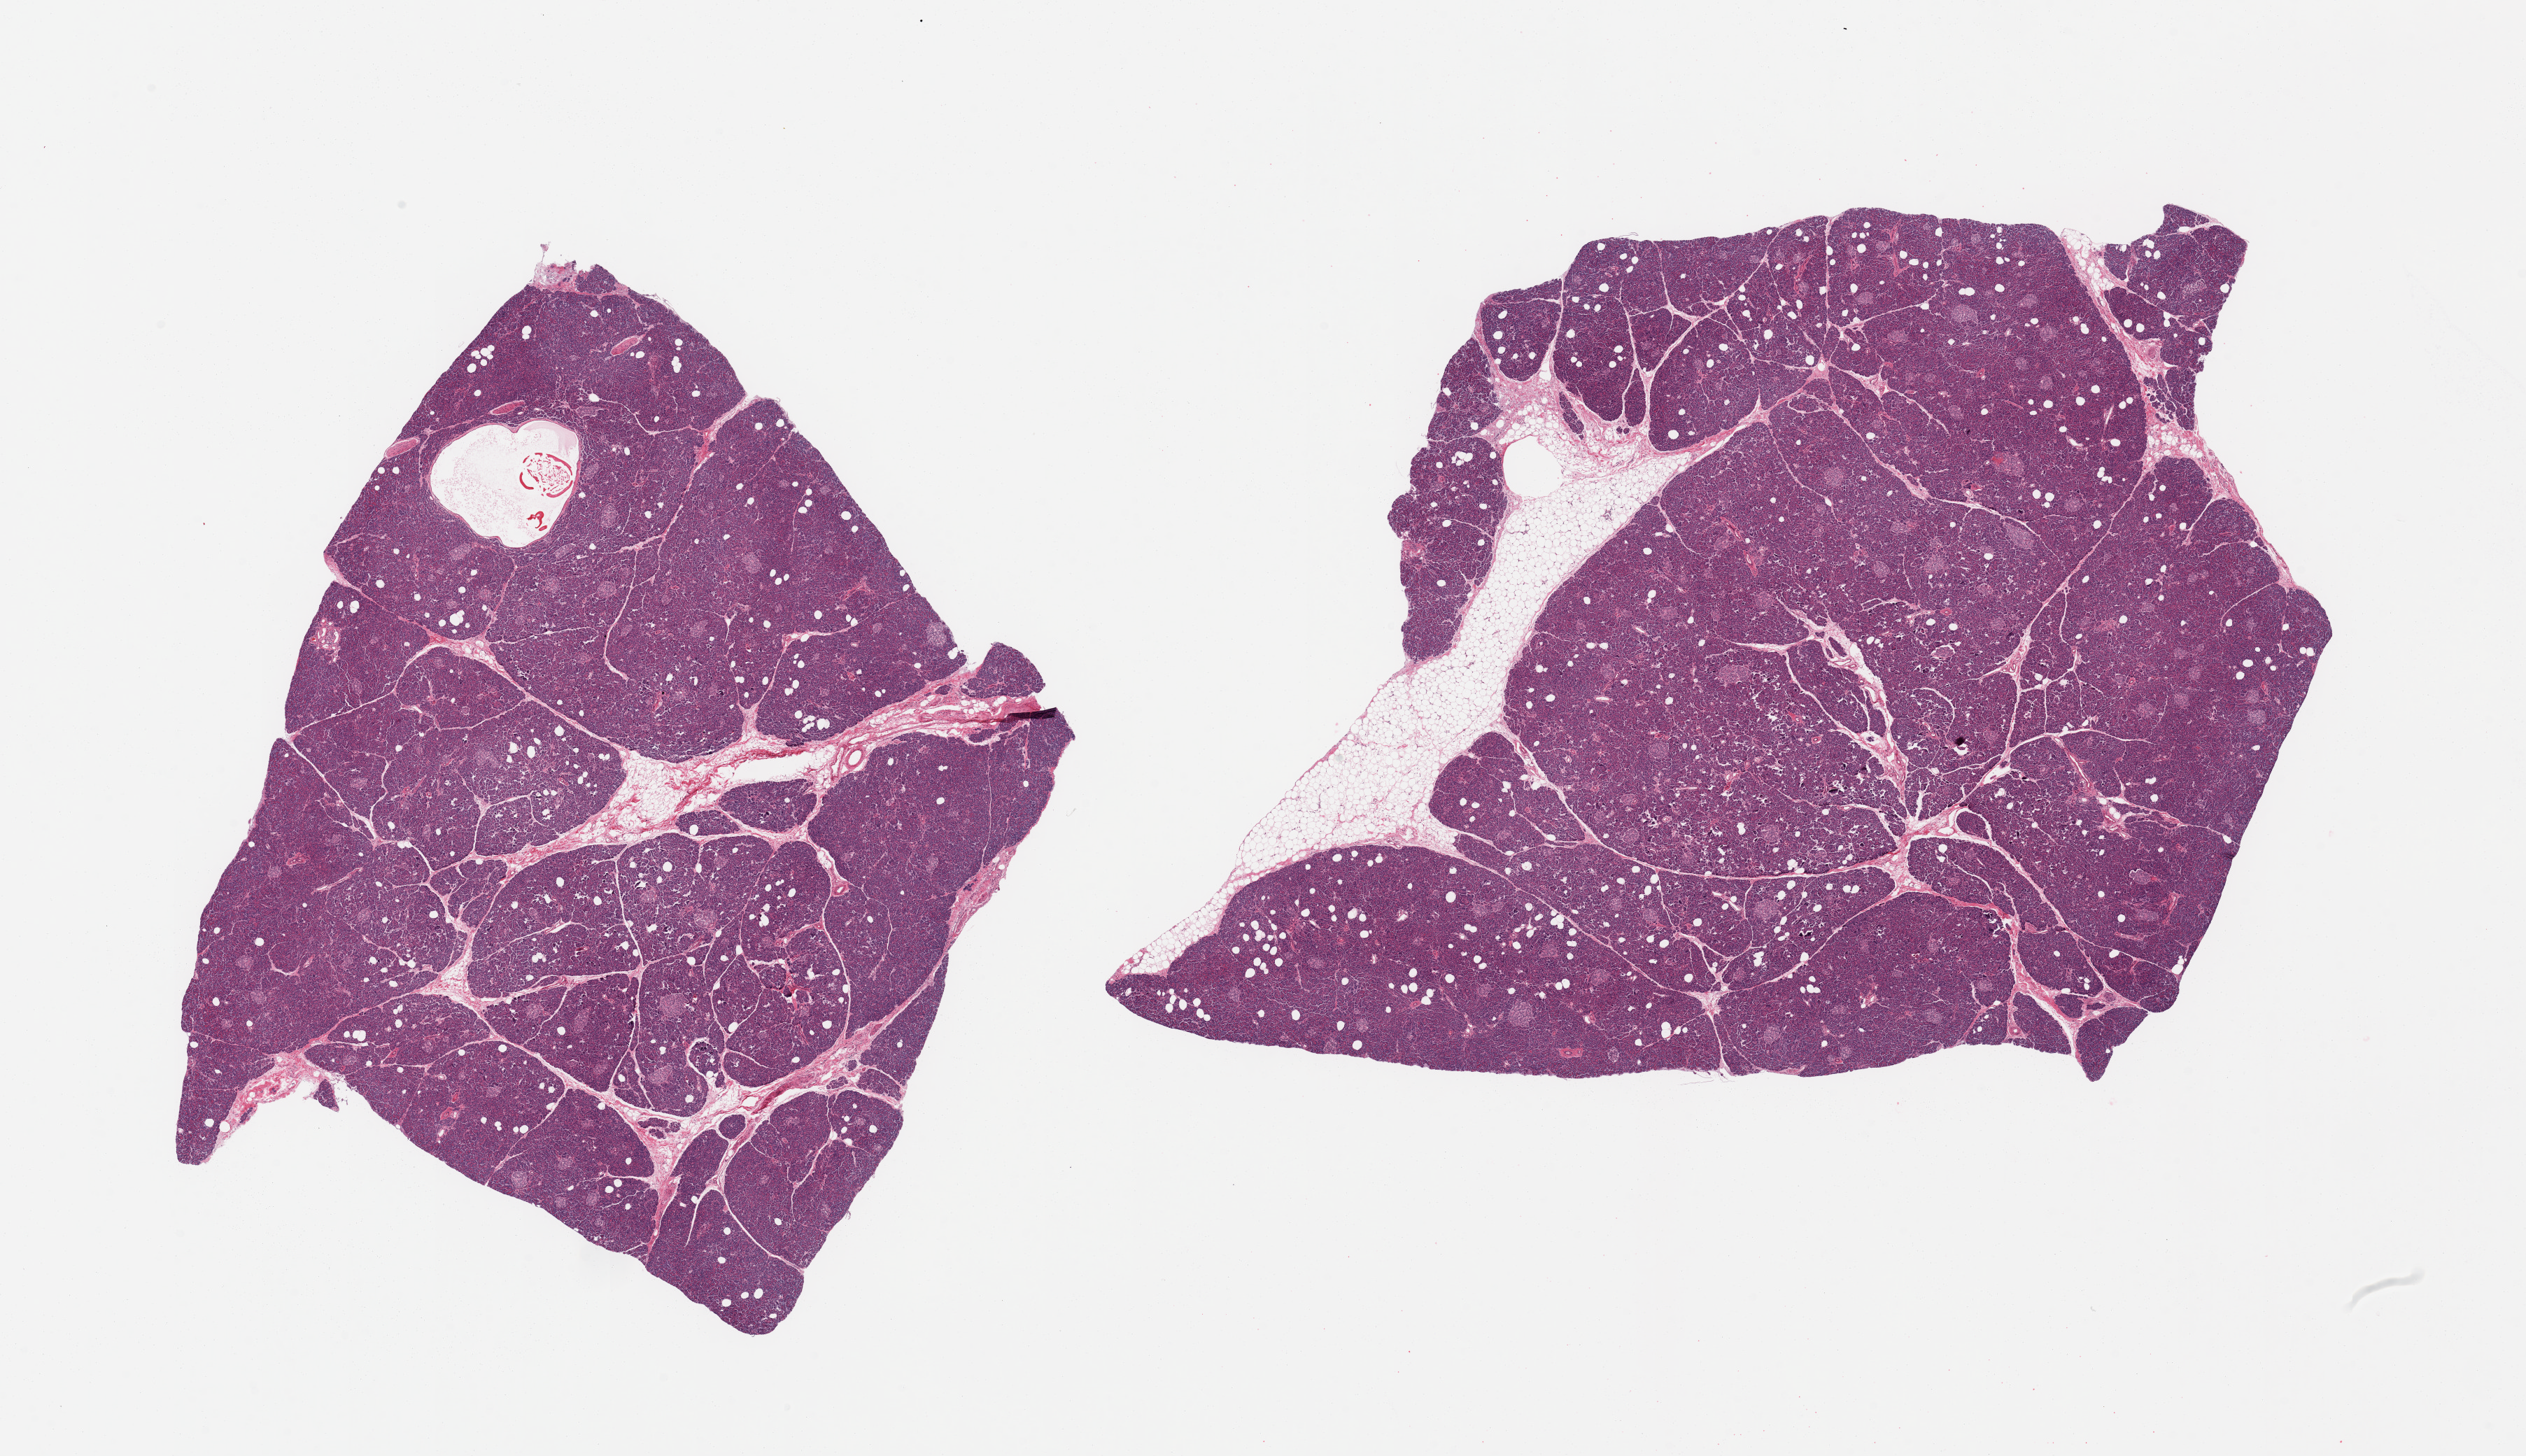
Haematoxylin and eosin whole-slide image, shown as a low-resolution overview of the whole scanned area (about 28.5 x 16.5 mm, slide scanned at 20x). PAXgene-fixed paraffin-embedded (PFPE) section. Sampled site (target tissue): pancreas. Tissue donor sample. Donor sex: female.
Pathologist's review note for this sample: 2 pieces; 10% external and internal fat; plentiful endocrine islets.